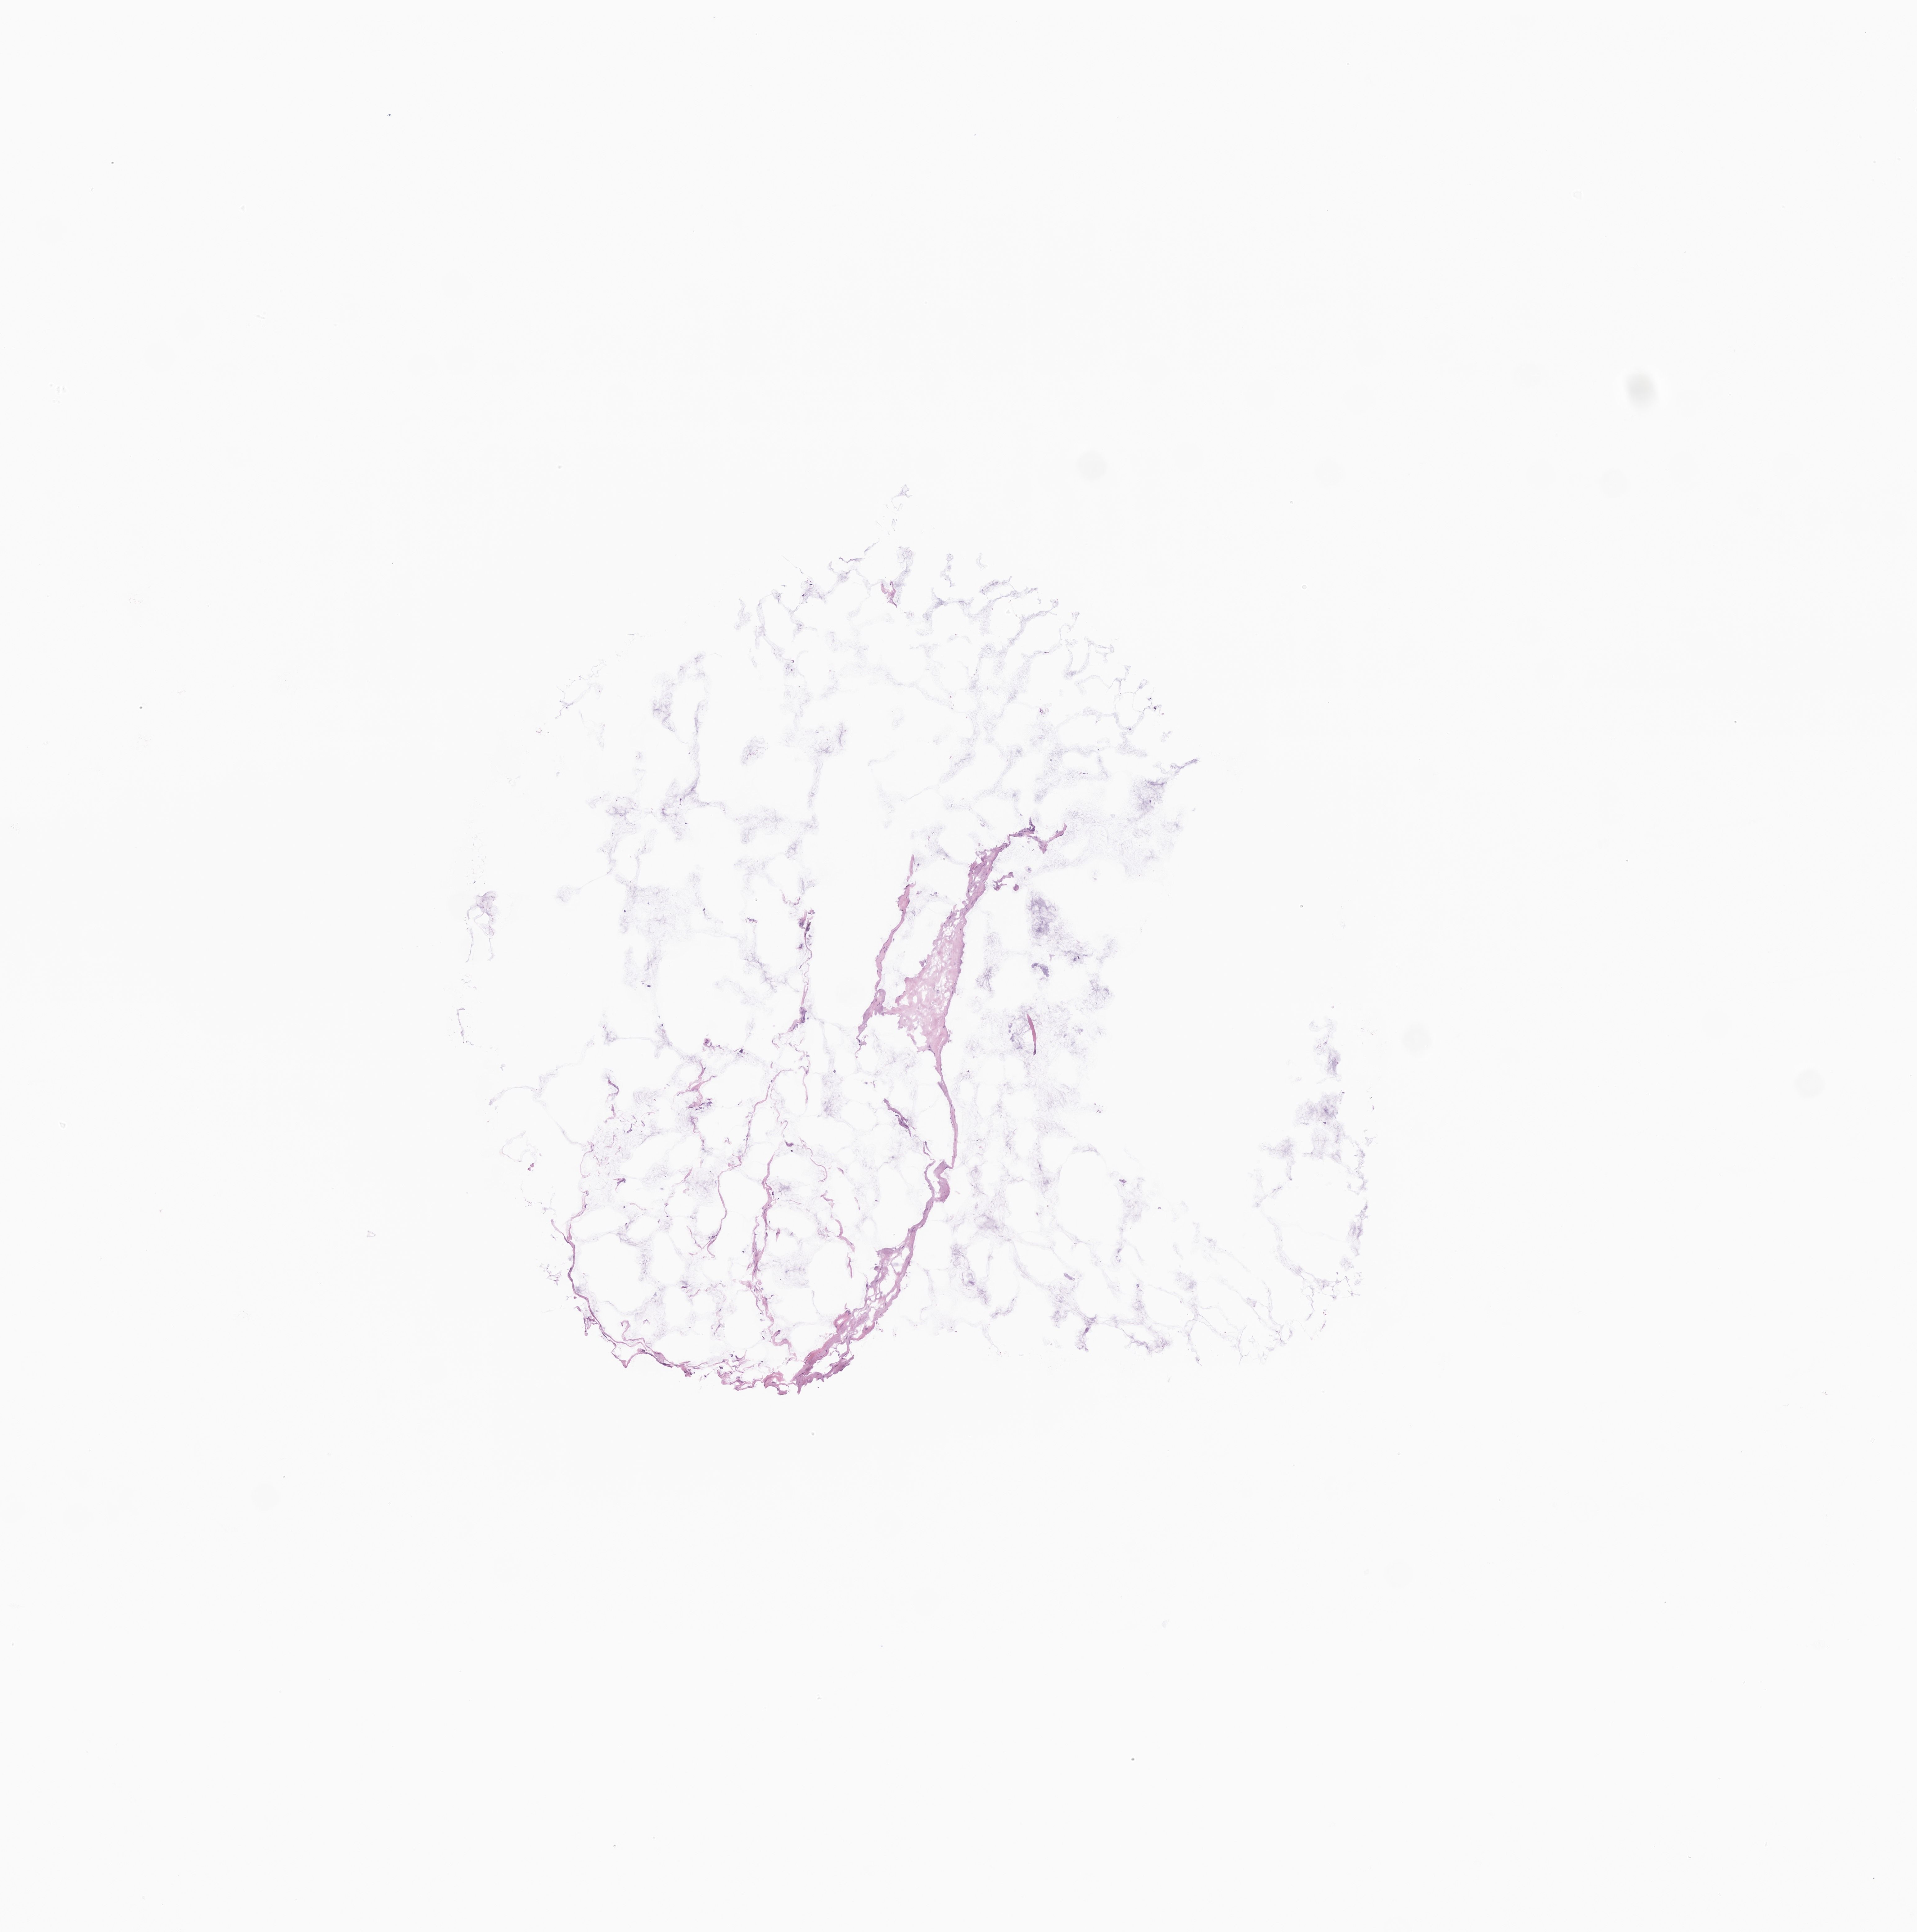
Whole-slide image, H&E stain — low-resolution overview of the scanned area, about 6.5 x 6.6 mm; cryosection; primary tumor; site: breast (left). Female, age 73 years at initial diagnosis. Pathologist review of this section (percent, as recorded): tumor cells 1%, tumor nuclei 30%, stromal cells 99%, necrosis 0%, normal cells 0%. Infiltration values recorded for this section: lymphocyte infiltration 2%, monocyte infiltration 1%, neutrophil infiltration 0%.
Histologic diagnosis: Infiltrating duct carcinoma, NOS. Section: top of the tissue portion.